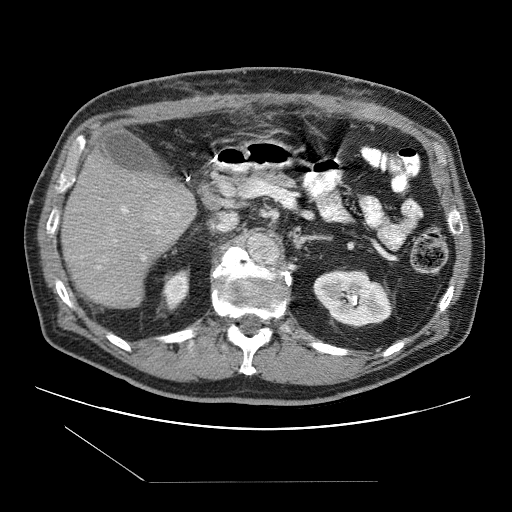
Contrast-enhanced abdominal CT (liver protocol), one axial slice. Slice 47 of 109 in the series (ordered by position). One of 2 acquisitions stored at this slice position. Soft-tissue window (W 400 / L 40 HU). 2.5 mm slice thickness. 512 × 512 image matrix, field of view 400 × 400 mm. From the clinical record (not read from this slice): diagnosis: hepatocellular carcinoma (patient treated with transarterial chemoembolisation; whether this scan precedes or follows treatment is not stated here); TNM stage (as recorded): Stage-IIIB; Child-Pugh class: A; tumour differentiation: well differentiated; tumour nodularity: multinodular.
Annotated regions visible in this slice (semi-automatic segmentation, software-assisted and operator-edited):
- liver parenchyma outside the tumour (the mass and vessels are separate outlines, so this box may not span the whole liver): box from (x=60, y=150) to (x=196, y=308) px
- liver vessels: (x=98, y=207)–(x=160, y=268)